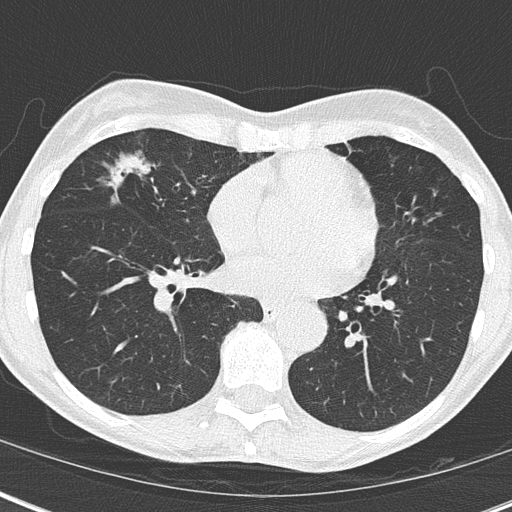
Chest CT (low-dose screening protocol), one axial image, third annual screen, lung window (W 1500 / L -600 HU), lung (sharp) reconstruction kernel (B50f), slice 102 of 173 in the series, 512 × 512 image matrix, field of view 290 × 290 mm. Female, age 67 years at enrolment. Current smoker at enrolment.
Expert-annotated lung lesion, bounding box (x1, y1, x2, y2) in pixels: (93, 142, 192, 231). Screening reader's record for this exam (one nodule recorded; not confirmed to be the boxed lesion): non-calcified nodule or mass ≥4 mm, right middle lobe, 32 × 17 mm, mixed attenuation, pre-existing on the prior screen: yes; interval growth: yes. Official screen result: positive, other. Lung cancer was diagnosed 76 days after this screen: bronchiolo-alveolar adenocarcinoma, NOS, right middle lobe, well differentiated (G1), stage IA (AJCC 6th edition), 25 mm at pathology.